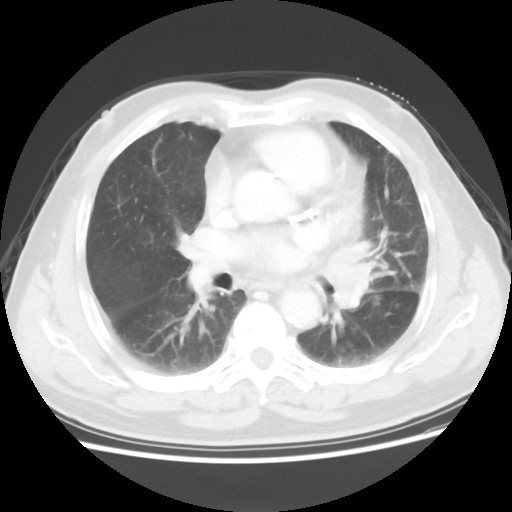
Chest CT, one axial slice. Position 31 of 56 along the scan axis. Reconstruction kernel STANDARD. Lung window (W 1500 / L -600 HU). 5 mm slice thickness. 512 × 512 image matrix. Patient: male, 75 years. From the clinical record (not read from this slice): clinical TNM (as recorded): T3 N0 M0.
Outlined on this slice (rectangle marked by the reading radiologist):
- lung tumour (recorded histology: squamous cell carcinoma): box from (x=320, y=222) to (x=387, y=321) px